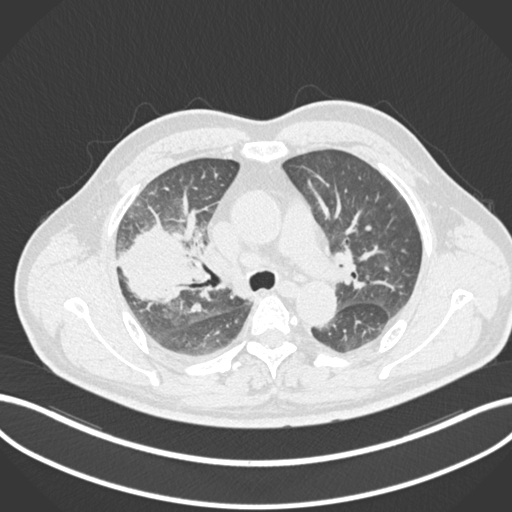
Chest CT, one axial slice. Slice 653 of 852 in the series (ordered by position). Reconstruction kernel B30f. 120 kVp. Lung window (W 1500 / L -600 HU). 1 mm slice thickness. 512 × 512 image matrix. Patient: male, 55 years. Case-level facts recorded for this patient, not image findings: clinical TNM (as recorded): T3 N2 M1.
Structures marked on this image (bounding box drawn by a radiologist):
- lung tumour (recorded histology: adenocarcinoma): box from (x=113, y=219) to (x=187, y=306) px